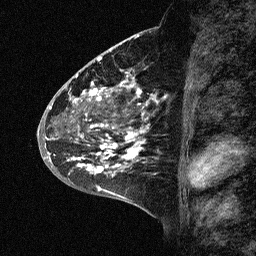
Breast MRI (dynamic contrast-enhanced), one sagittal slice. Position 28 of 64 along the scan axis. Dynamic contrast-enhanced study with each time point stored as its own series, time point 2 of 3 at this slice position (early post-contrast, ordered by acquisition time). 1.5 T. TE 4.5 ms, TR 11 ms. 2.06 mm slice thickness. 256 × 256 image matrix. Patient: female, 46 years. From the clinical record (not read from this slice): setting: breast cancer imaged before/during neoadjuvant chemotherapy; receptor status: HER2-positive.
Outlined on this slice (semi-automatic segmentation, software-assisted and operator-edited):
- analysis volume of interest (the breast-tissue region the enhancement analysis was run in; not a lesion): bounding box <43,72,174,177> (left, top, right, bottom; pixels)
- tumour enhancement mask (voxels above the 90 % enhancement threshold inside the analysis volume of interest): <48,72,155,177>